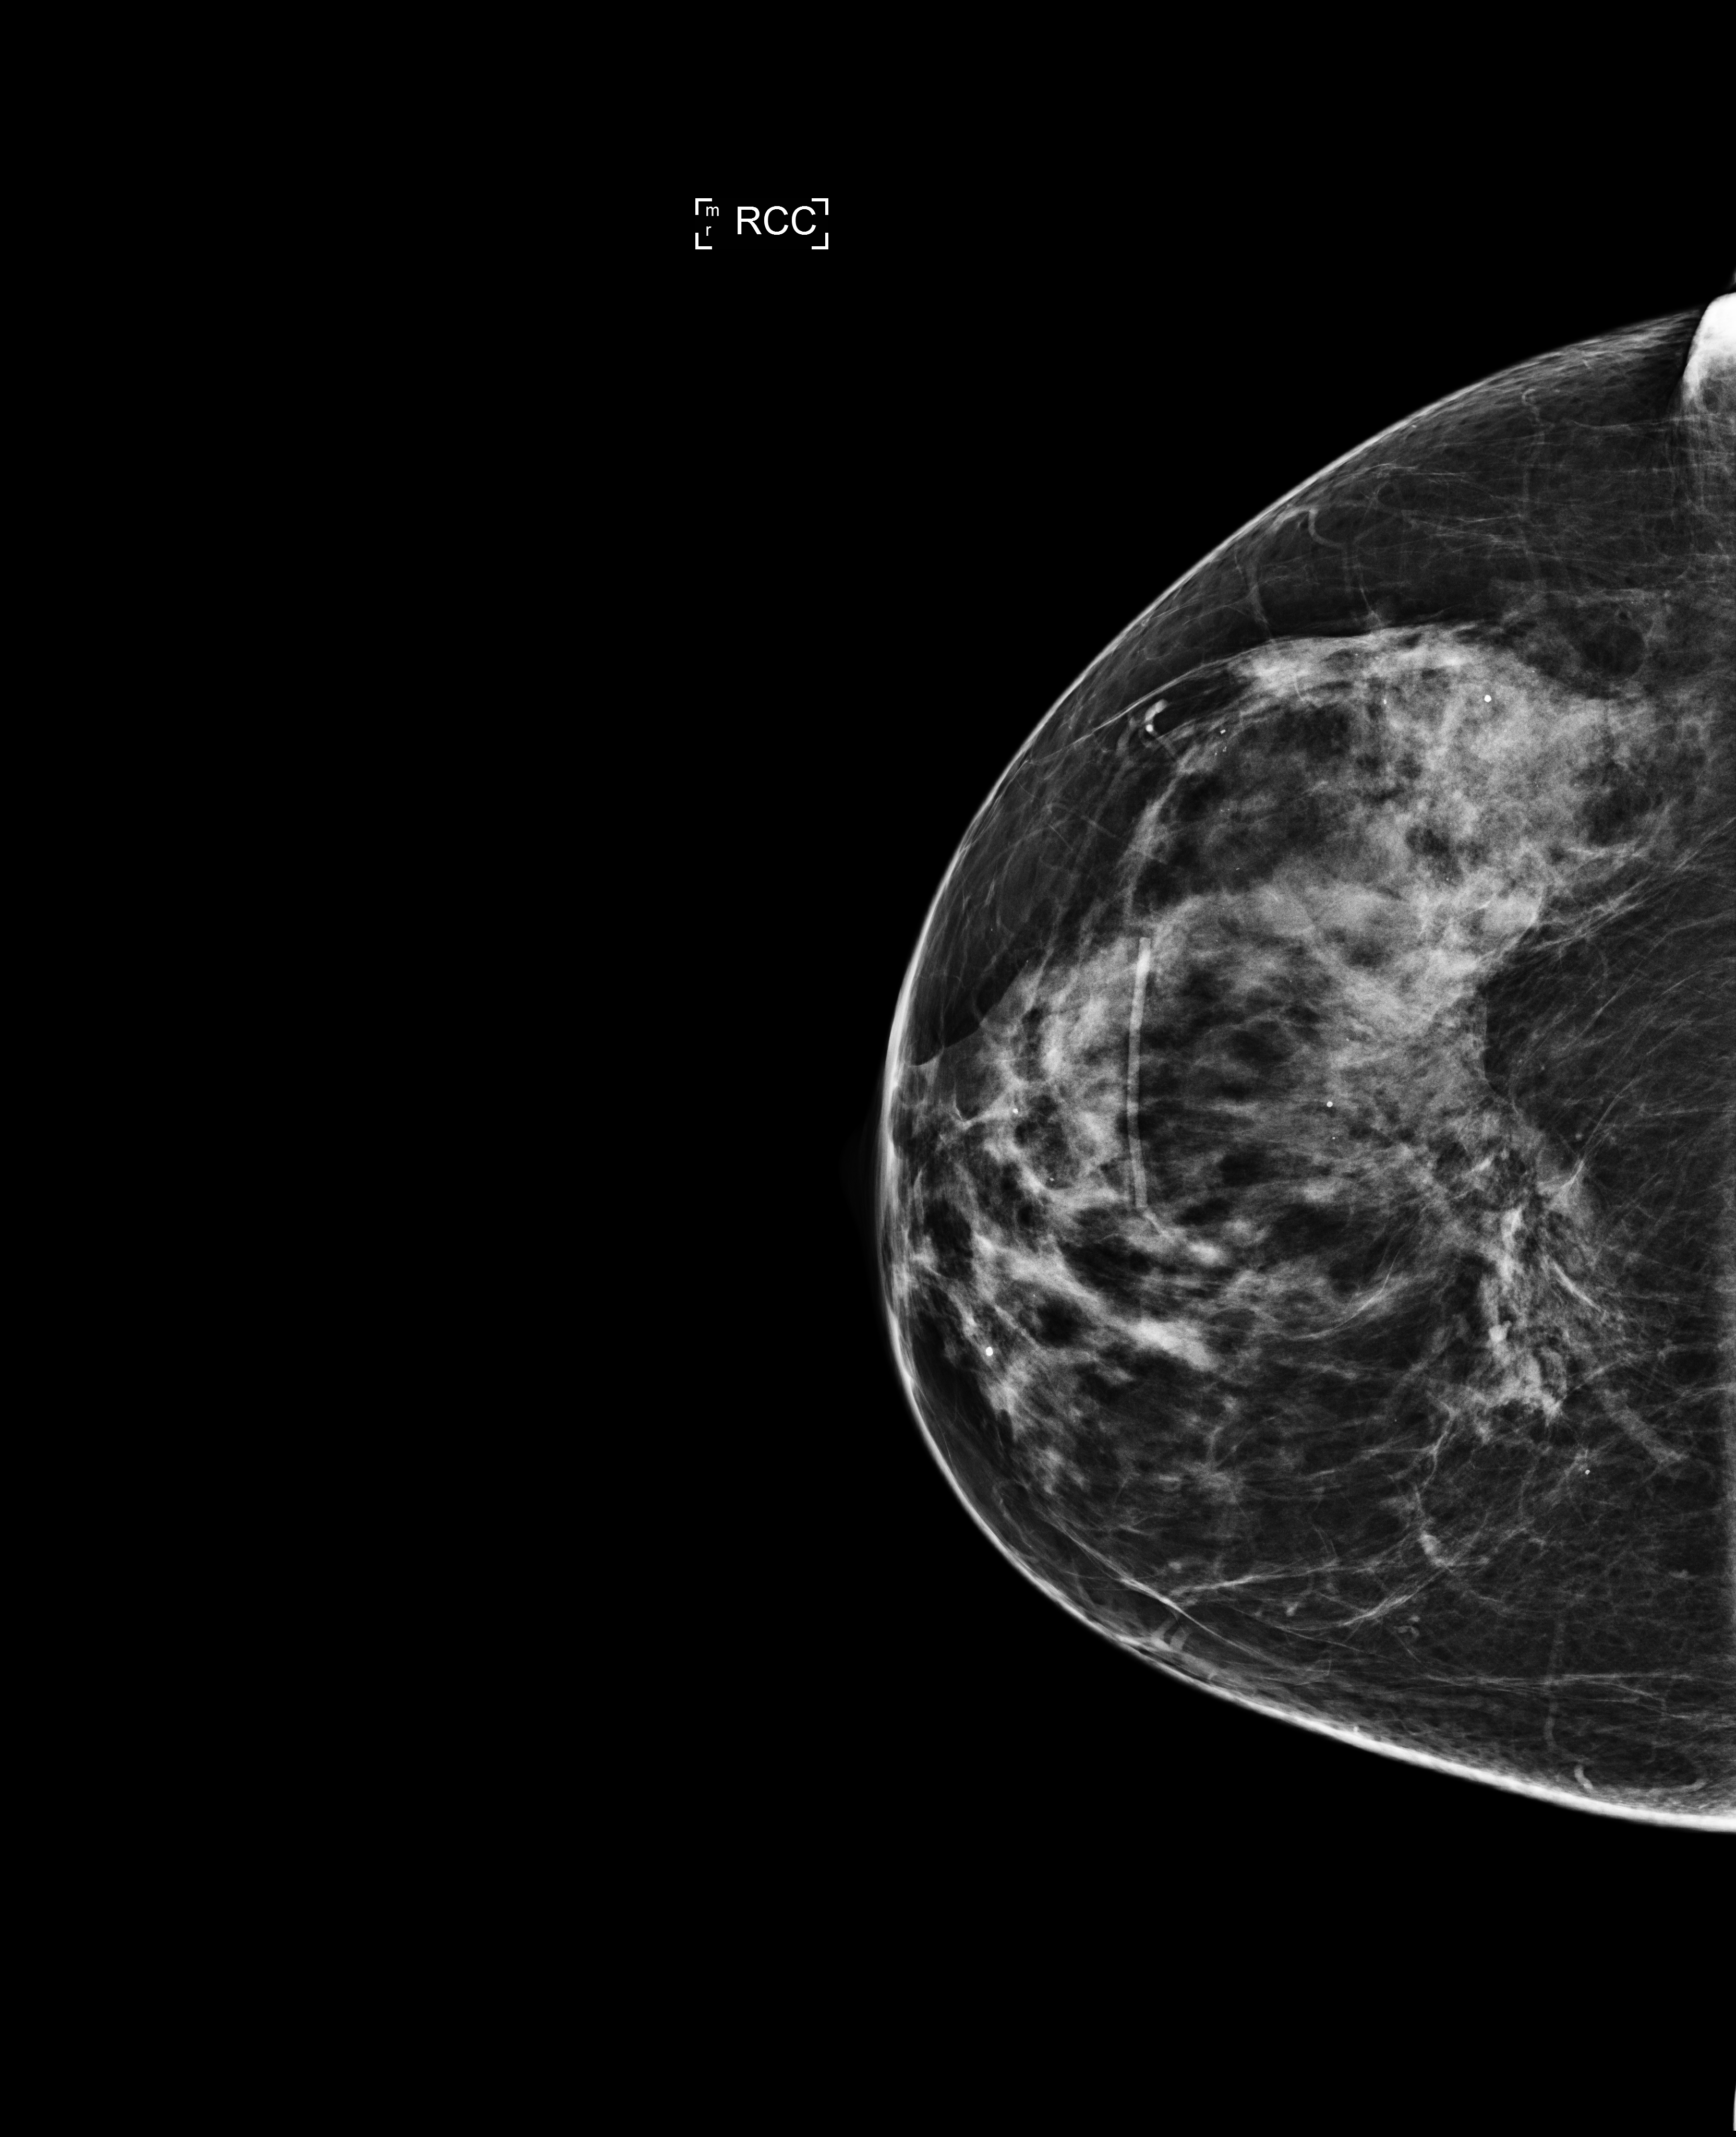
Screening examination, compressed breast thickness 69 mm. Patient: female, 60 years.
Image type: full-field digital mammogram. Breast: right. Projection: CC view.